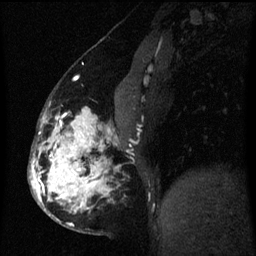
Breast MRI (dynamic contrast-enhanced), one sagittal slice. Dynamic contrast-enhanced series, image 2 of 3 at this slice position (ordered by acquisition). 1.5 T. TE 4.2 ms, TR 8 ms. 2 mm slice thickness. 256 × 256 image matrix, field of view 190 × 190 mm. Female patient, age 50 years.
Structures marked on this image (semi-automatically segmented with operator editing):
- analysis volume of interest (the breast-tissue region the enhancement analysis was run in; not a lesion): bounding box [x1, y1, x2, y2] px = [32, 107, 118, 231]
- tumour enhancement mask (voxels above the 70 % enhancement threshold inside the analysis volume of interest): [32, 109, 111, 226]